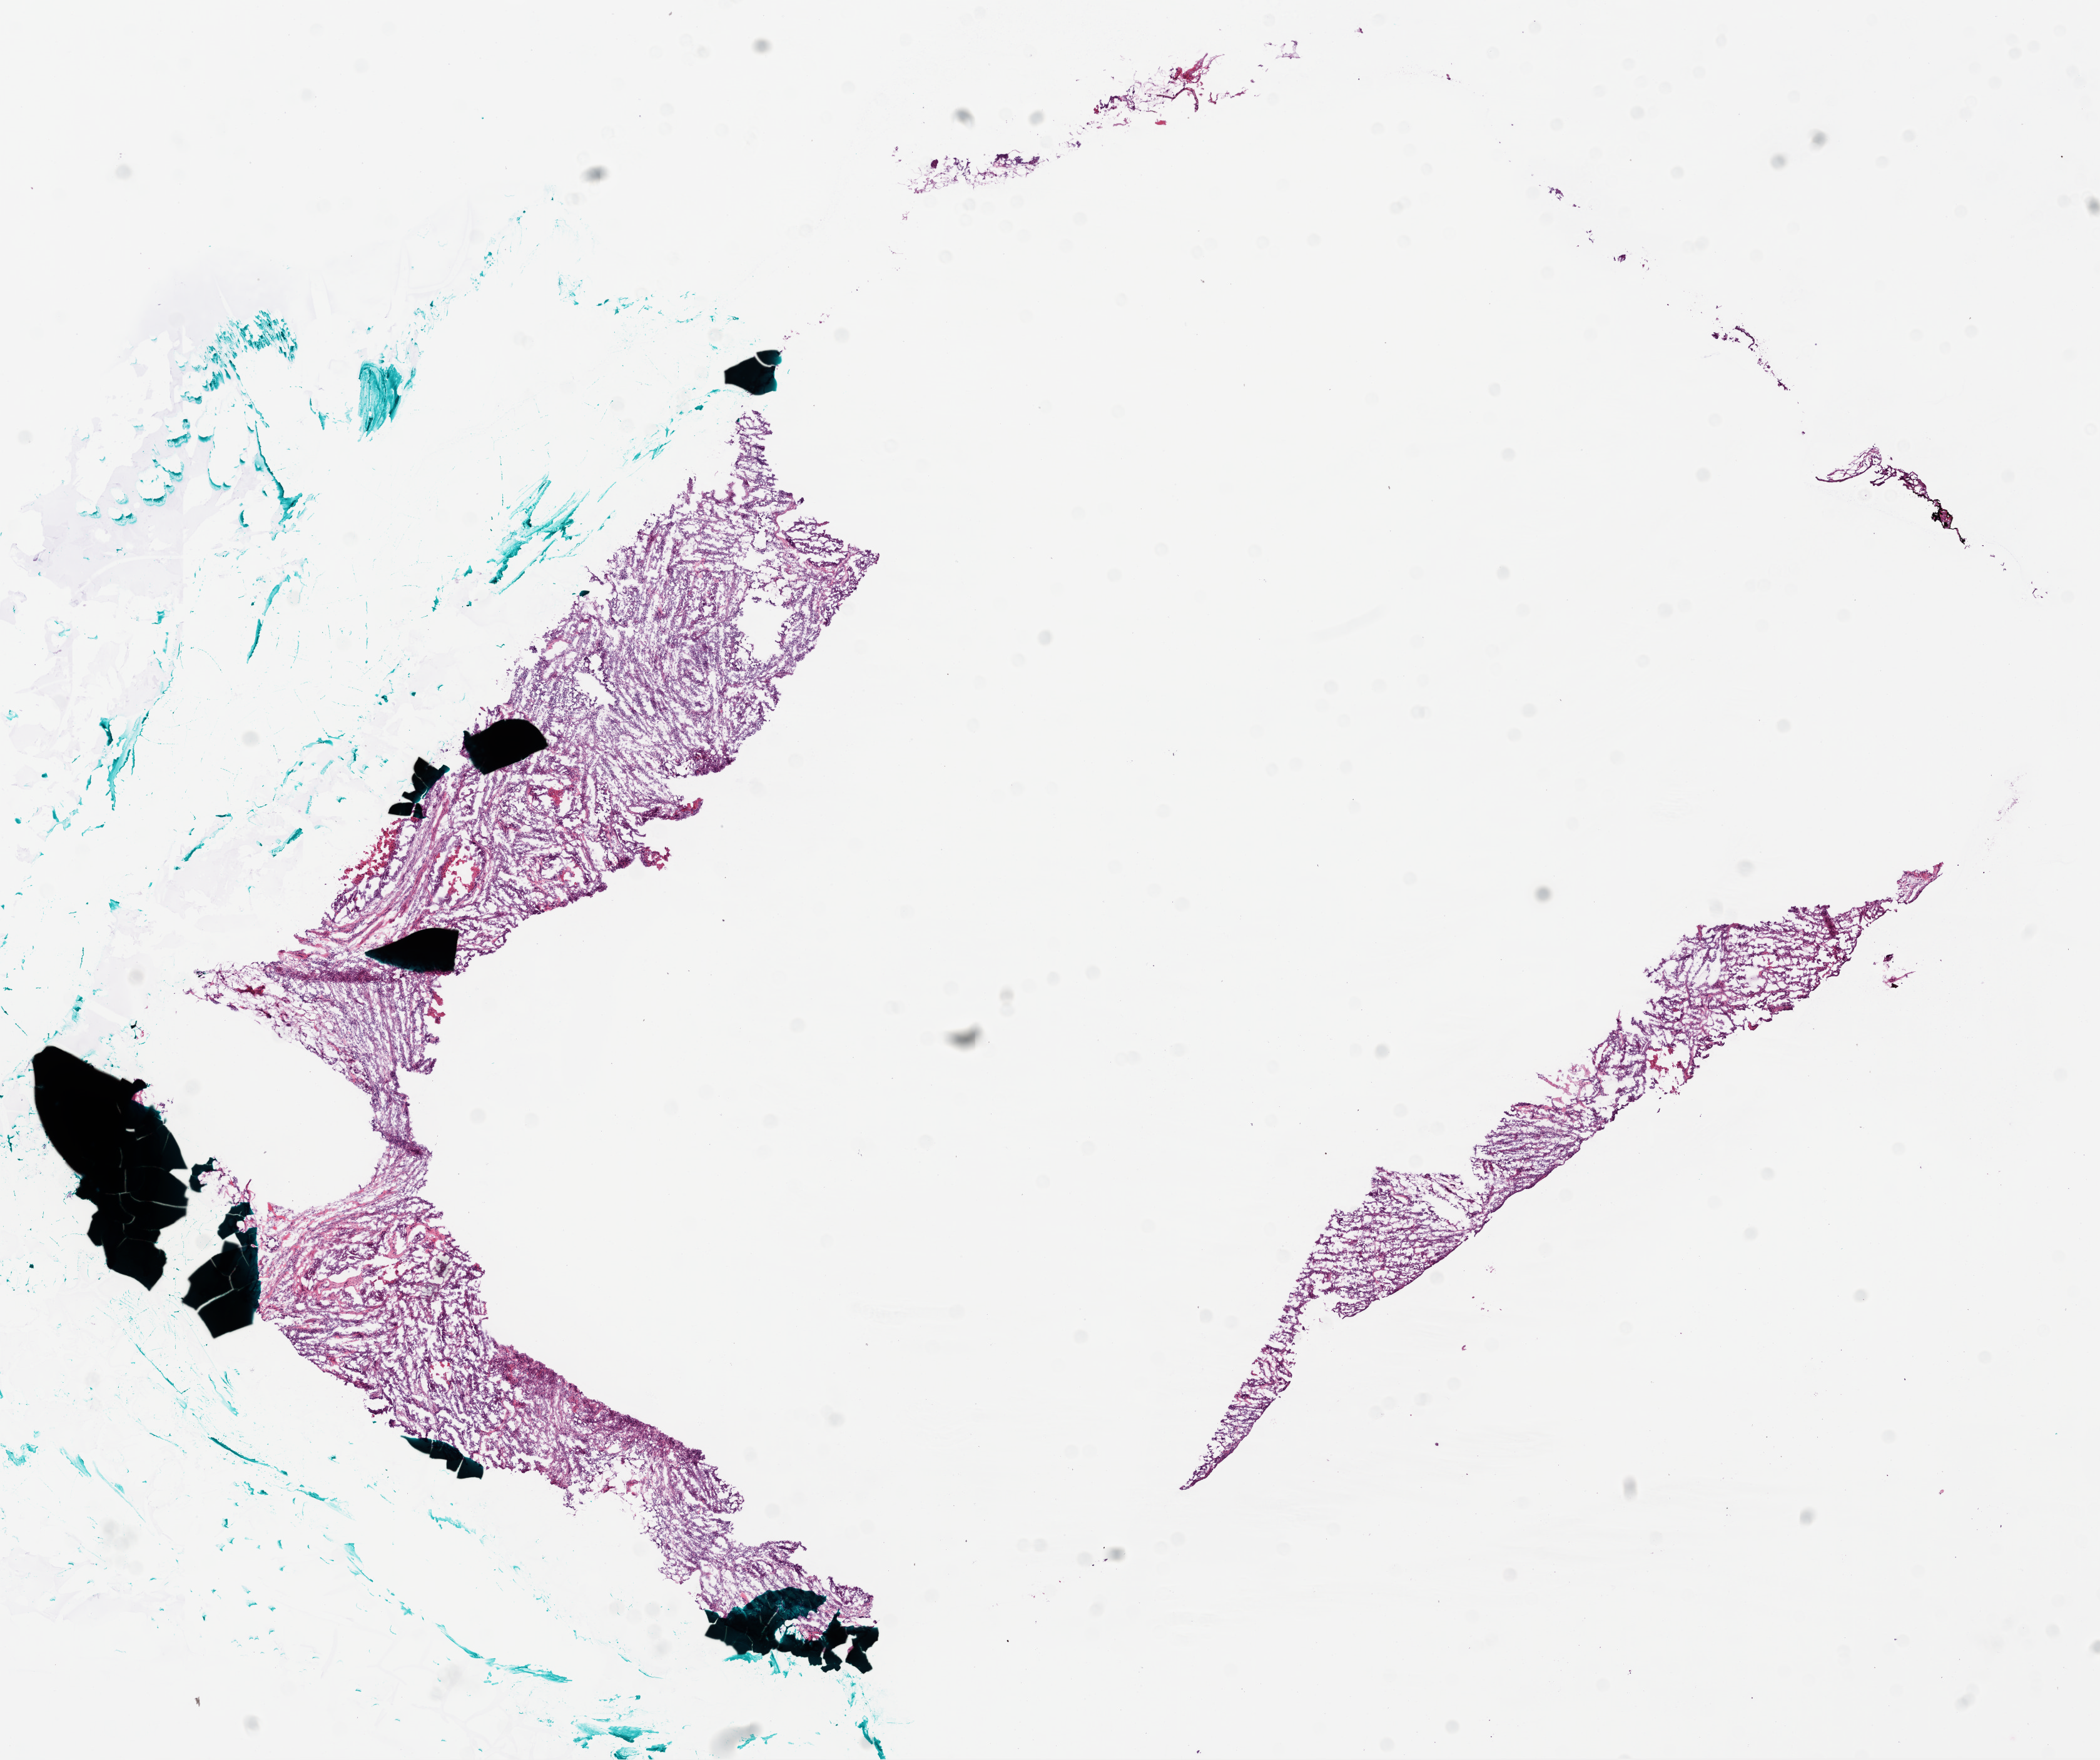
Digitized Hematoxylin and eosin (H&E) stained tissue section (whole slide) — shown as a low-resolution overview of the whole scanned area (about 13.5 x 11.3 mm); frozen section from the bottom of the tissue portion; sample: primary tumour, ovary. Female patient; age at initial diagnosis 73 years. Histologic grade: G3 (poorly differentiated). Composition of this section per pathologist review: tumour cells 85%, tumour nuclei 94%, normal cells 5%, stromal cells 1%, necrosis 9%.
Pathologic diagnosis: Serous cystadenocarcinoma, NOS. FIGO stage: IIIC.